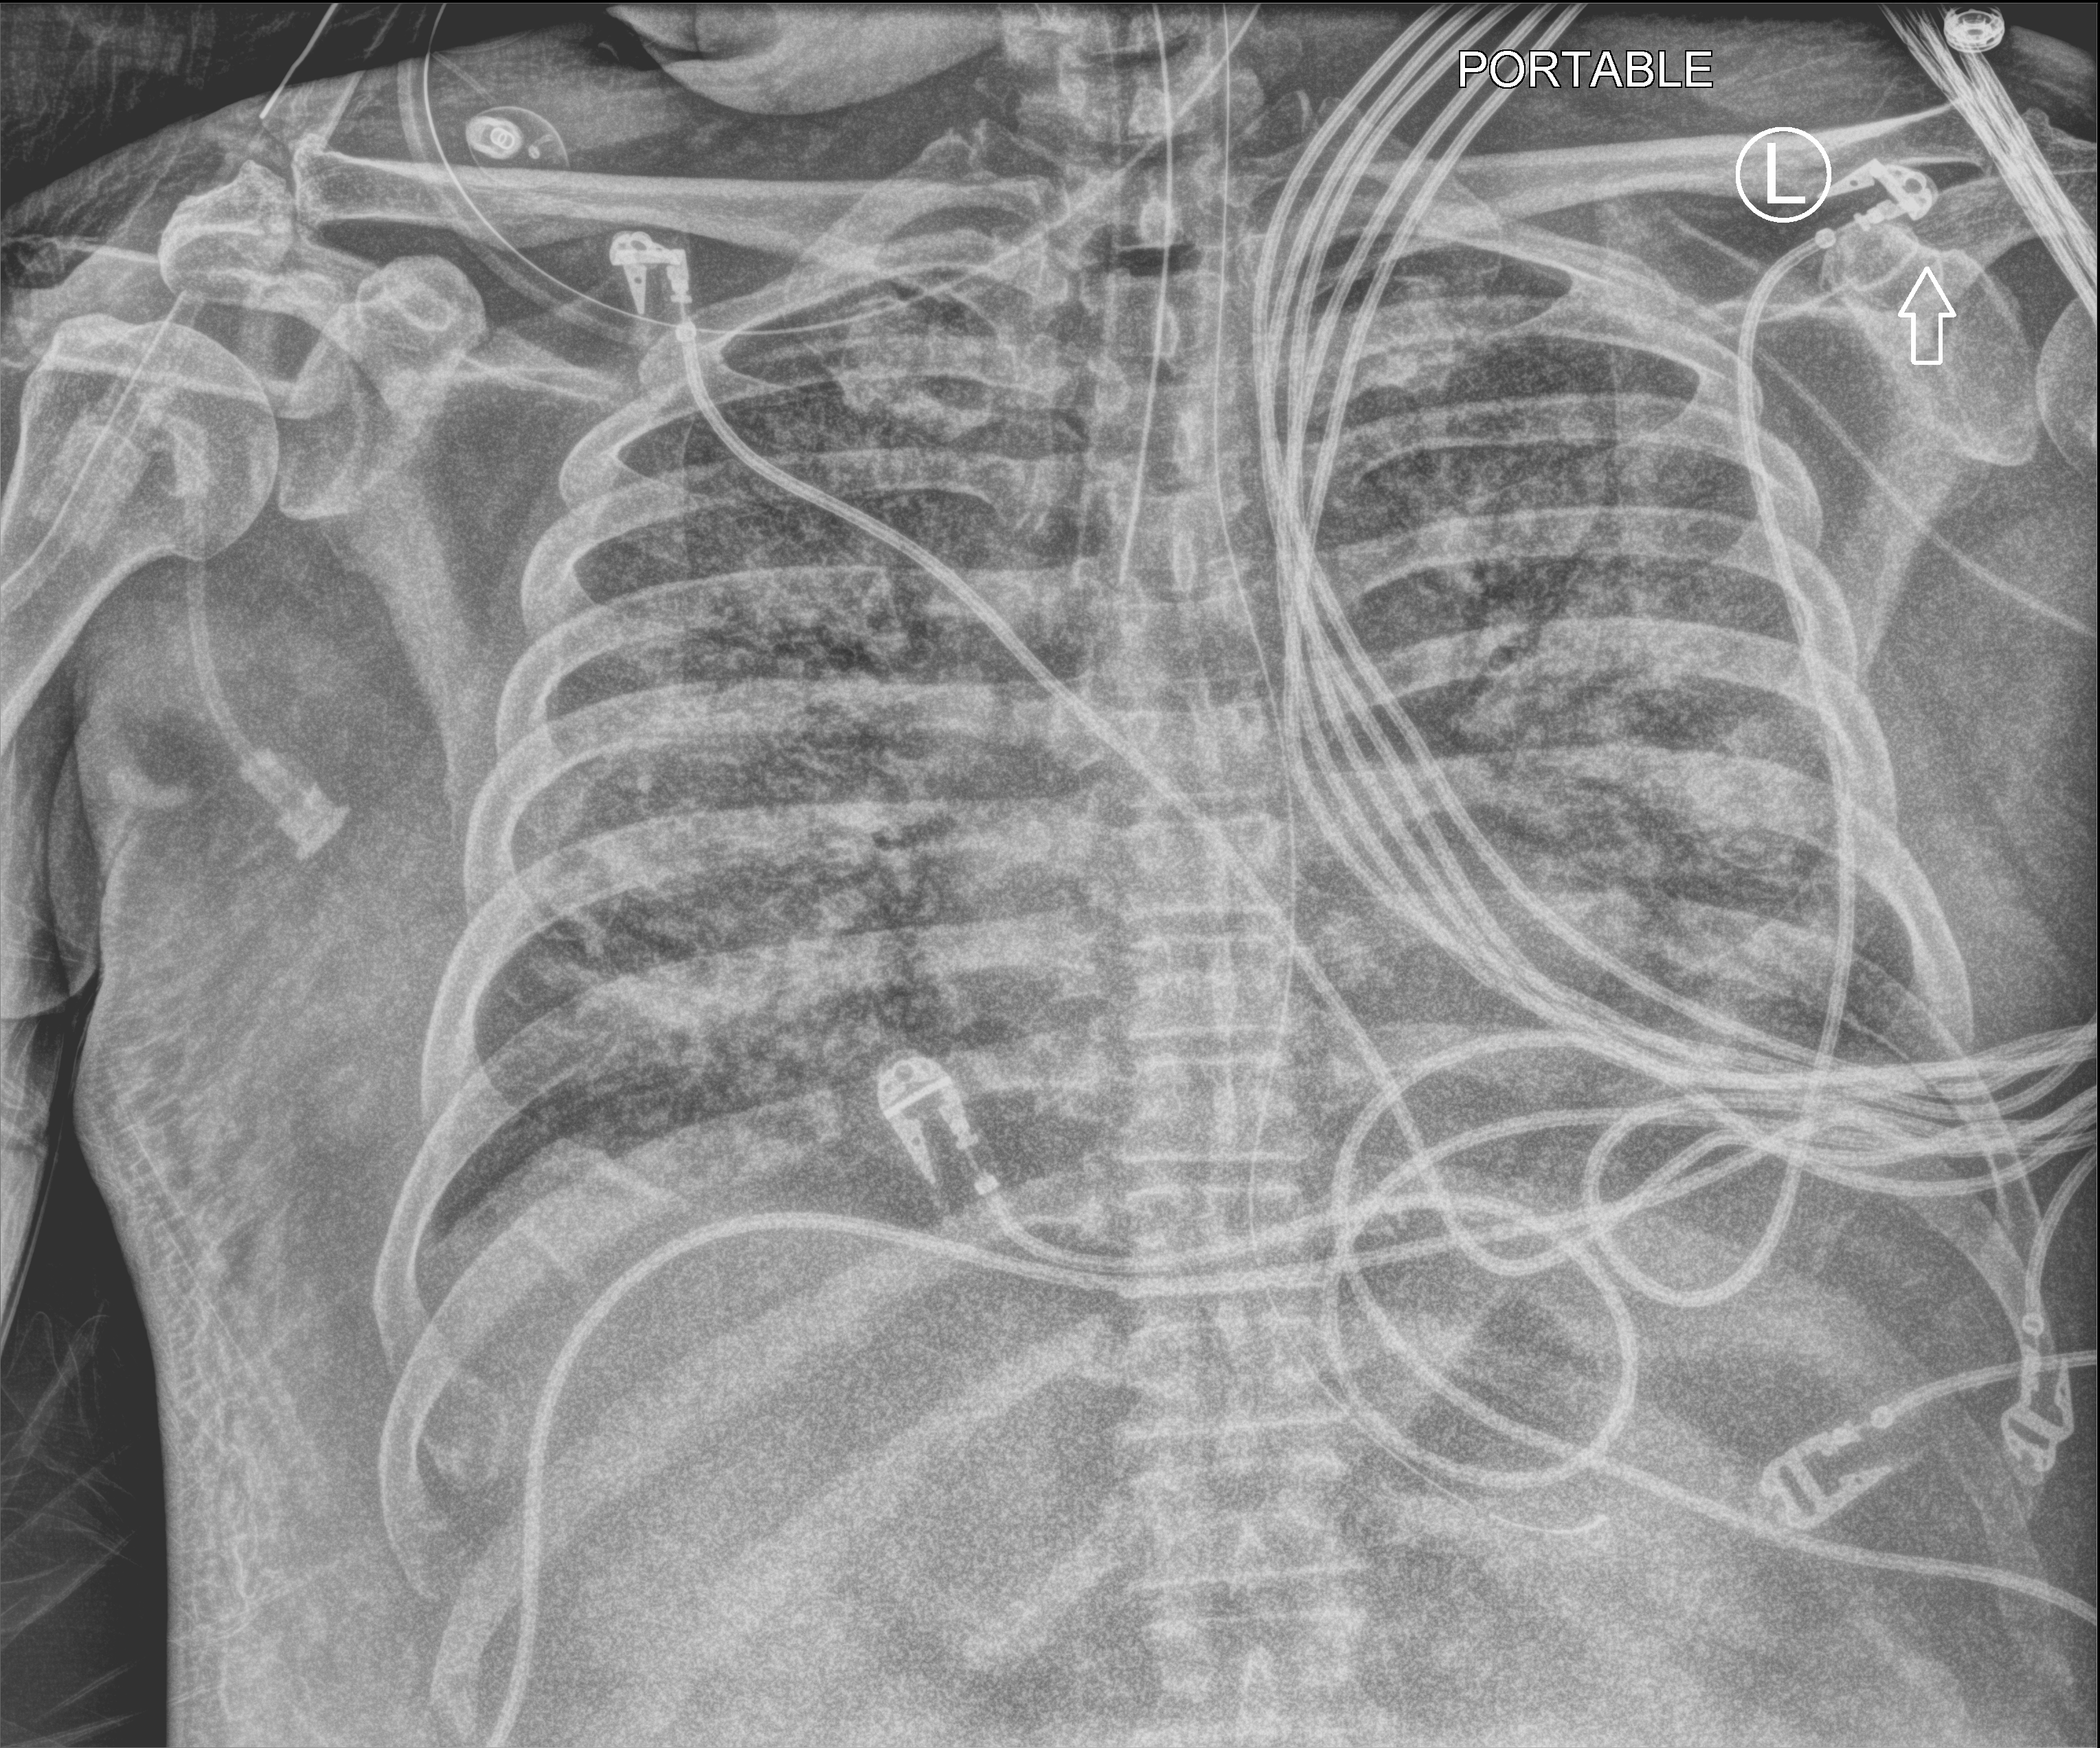
Chest X-ray (portable). Patient hospitalised with COVID-19; male, aged 60–74 years.
Admission-level facts for this patient (not findings on this image; timing relative to this image not recorded): mechanically ventilated during this hospital stay: yes; chronic kidney disease (admission record): no.